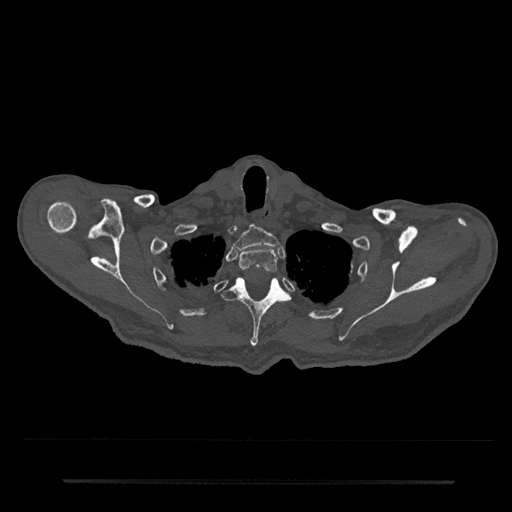
CT including the spine, one axial slice. Position 676 of 797 along the scan axis. Reconstruction kernel Br40s/3. Bone window (W 1800 / L 400 HU). 512 × 512 image matrix, field of view 427 × 427 mm. Patient: male, 74 years. Case-level facts recorded for this patient, not image findings: primary cancer: prostate.
Structures marked on this image (semi-automatically segmented with operator editing):
- T1 vertebra: box from (x=233, y=225) to (x=279, y=251) px
- T2 vertebra: (x=239, y=248)–(x=278, y=273)
- T3 vertebra: (x=221, y=277)–(x=291, y=347)